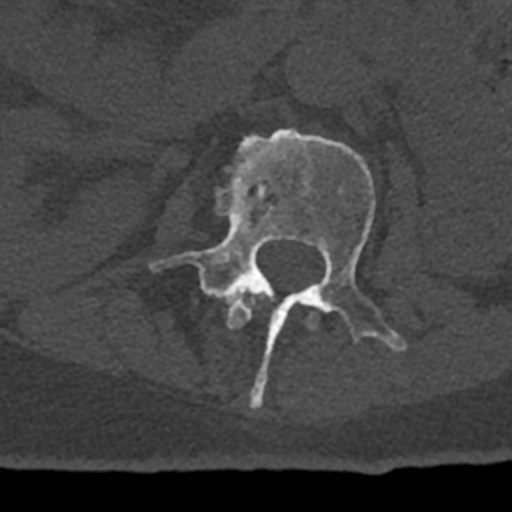
CT including the spine, one axial slice. Position 387 of 797 along the scan axis. Reconstruction kernel Br40s/3. Bone window (W 1800 / L 400 HU). 0.5 mm slice thickness. 512 × 512 image matrix, field of view 160 × 160 mm. Patient: male, 74 years. From the clinical record (not read from this slice): primary cancer: renal.
Structures marked on this image (semi-automatic segmentation, software-assisted and operator-edited):
- L1 vertebra: bounding box [x1, y1, x2, y2] px = [226, 290, 318, 329]
- L2 vertebra: [150, 128, 407, 408]